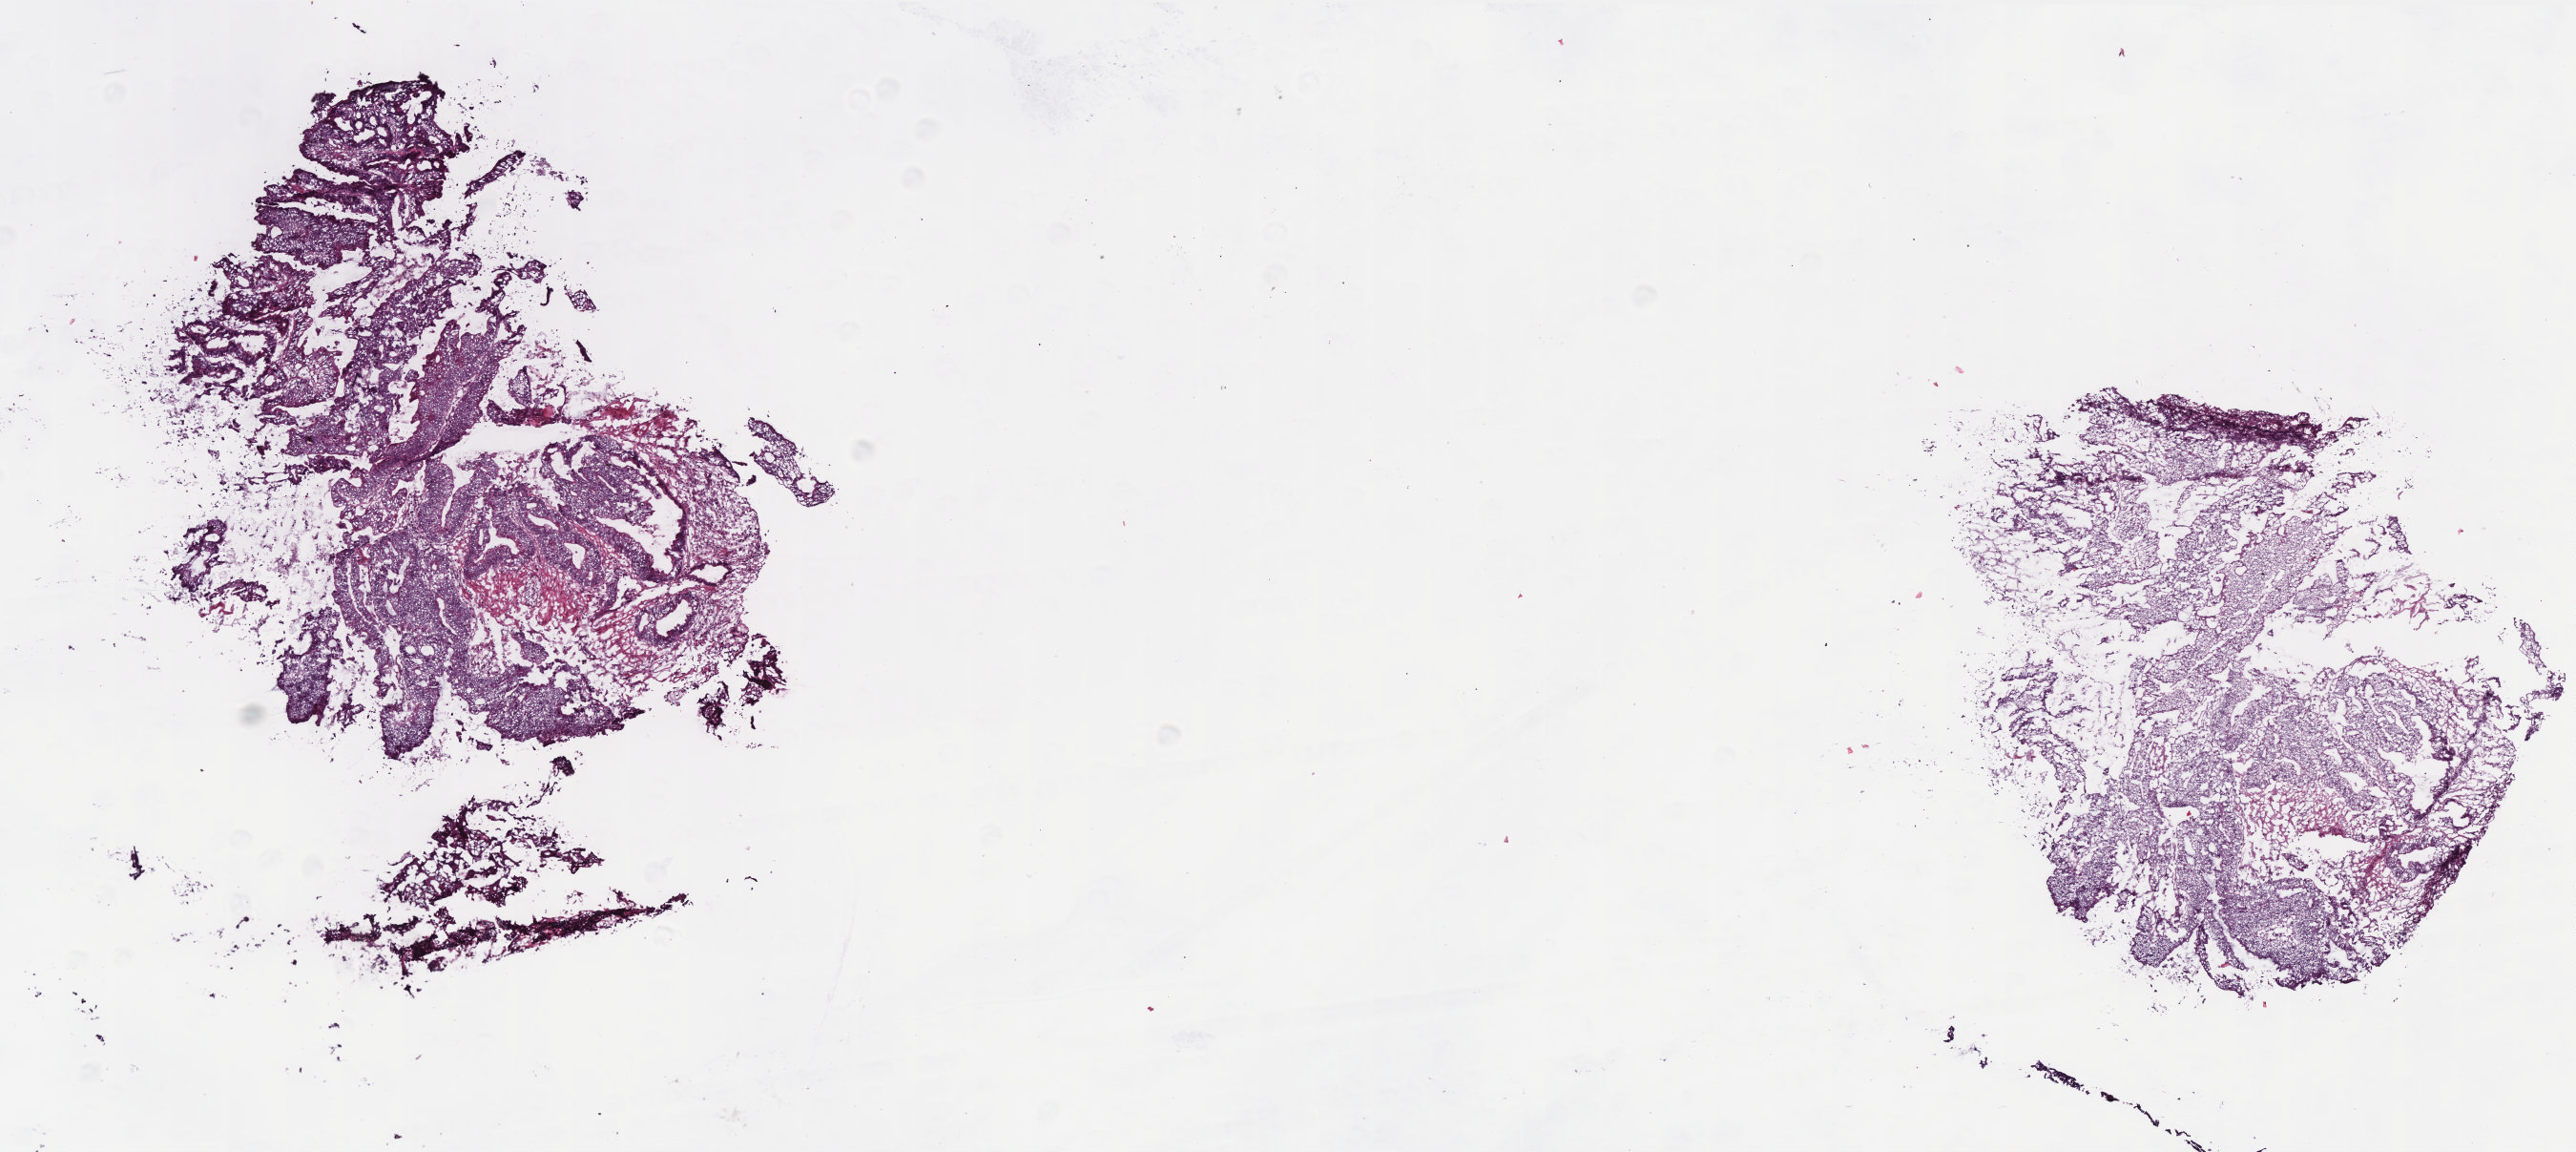
Whole-slide histology image, Hematoxylin and eosin (H&E) stained — a low-resolution overview of the entire scanned area, about 10.8 x 4.8 mm, frozen section, colon, primary tumour sample. Female, age 66 years at initial diagnosis. Pathologist review of this section (percent, as recorded): tumour cells 85%, tumour nuclei 90%, normal cells 0%, stromal cells 14%, necrosis 1%. Infiltration values recorded for this section: lymphocyte infiltration 4%, monocyte infiltration 1%, neutrophil infiltration 0%.
Histologic diagnosis: Adenocarcinoma, NOS (sigmoid colon). AJCC pathologic stage: IIIB (6th edition).